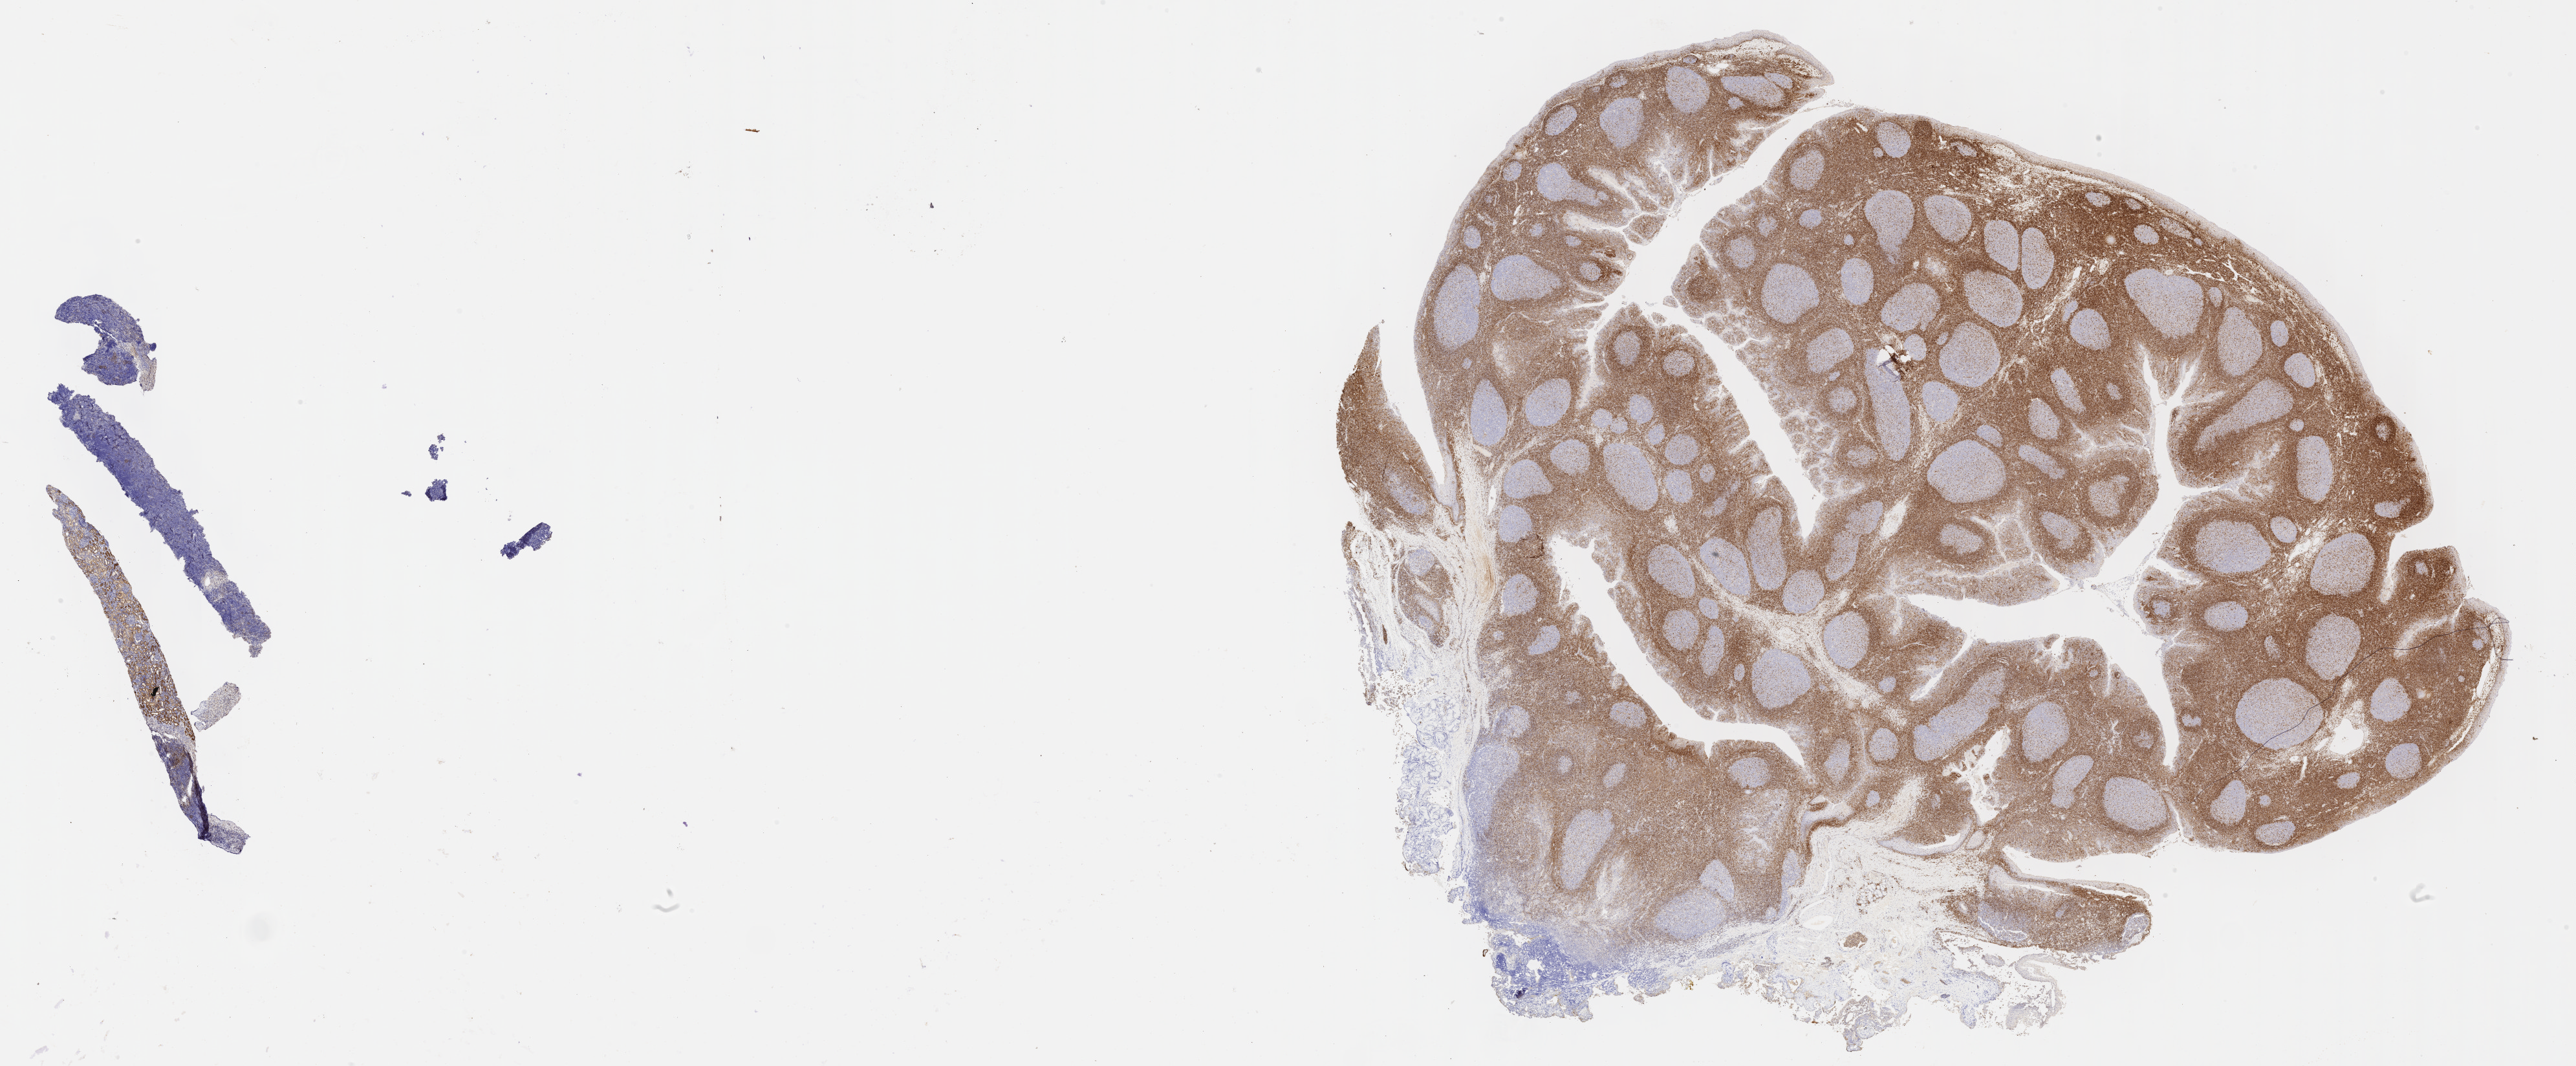
Immunohistochemistry (IHC) whole-slide image stained for BCL2 — shown as a low-resolution overview of the whole scanned area (about 32.2 x 13.3 mm). Tumor tissue. Anatomic site: liver. Male, age 8 years at initial diagnosis.
Diagnosis: Burkitt lymphoma, NOS.